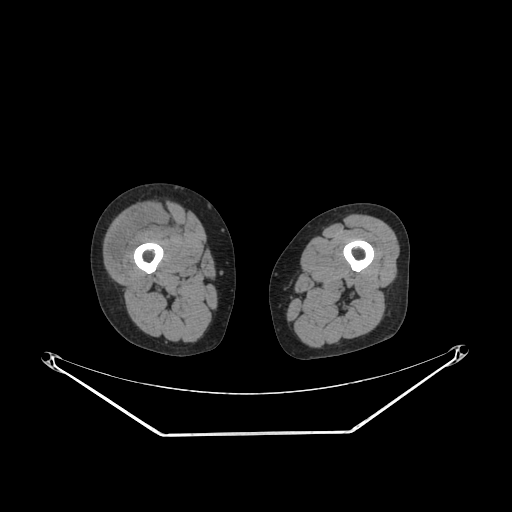
CT of an extremity soft-tissue mass (from a PET/CT study), one axial slice. Slice 219 of 311 in the series (ordered by position). Reconstruction kernel SOFT. 140 kVp. Soft-tissue window (W 400 / L 40 HU). 512 × 512 image matrix, field of view 500 × 500 mm. Female patient. From the clinical record (not read from this slice): histological type: pleiomorphic undifferentiated sarcoma; grade: high; site of the primary tumour: right quadricep.
Annotated regions visible in this slice (expert contour drawn on MRI and transferred to this co-registered scan by the dataset authors):
- tumour plus oedema (research contour): bounding box [x1, y1, x2, y2] px = [107, 206, 161, 270]